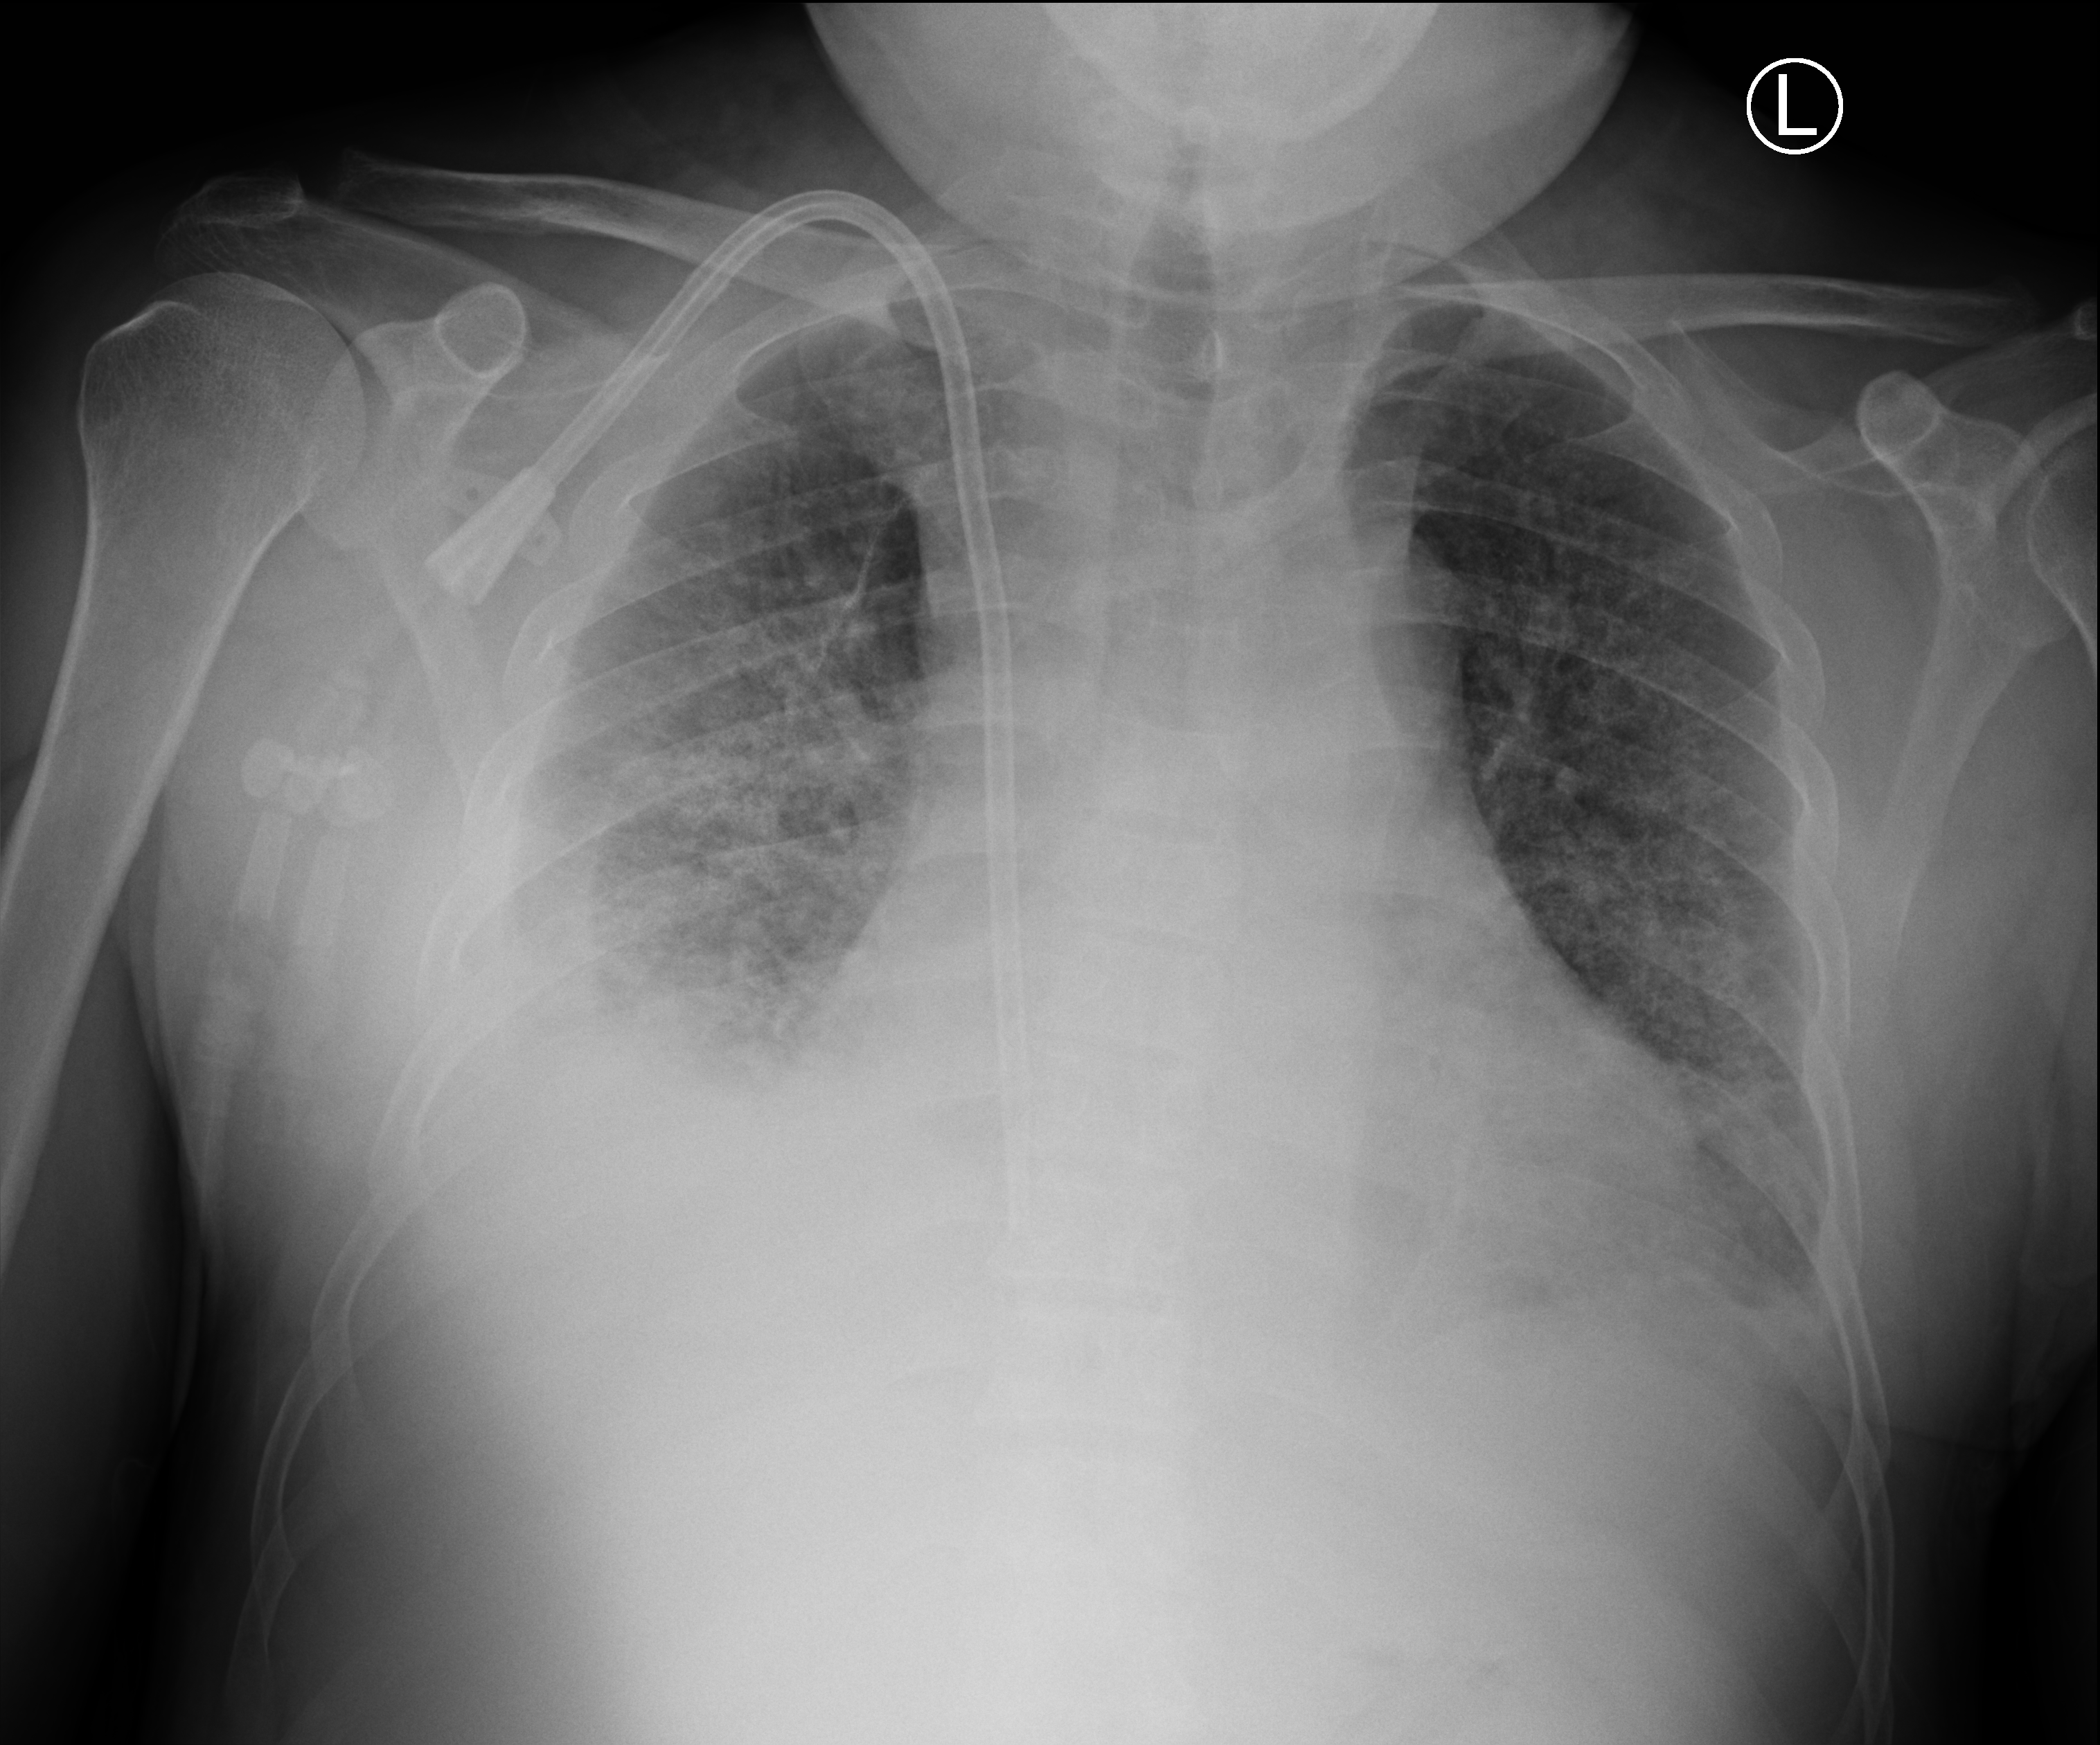
Chest X-ray (portable); anteroposterior (AP) projection. Male patient hospitalised with COVID-19, age 18–59 years.
Hospital-stay facts (about this admission, not read from this image; timing relative to this image not recorded):
- length of hospital stay: 7 days